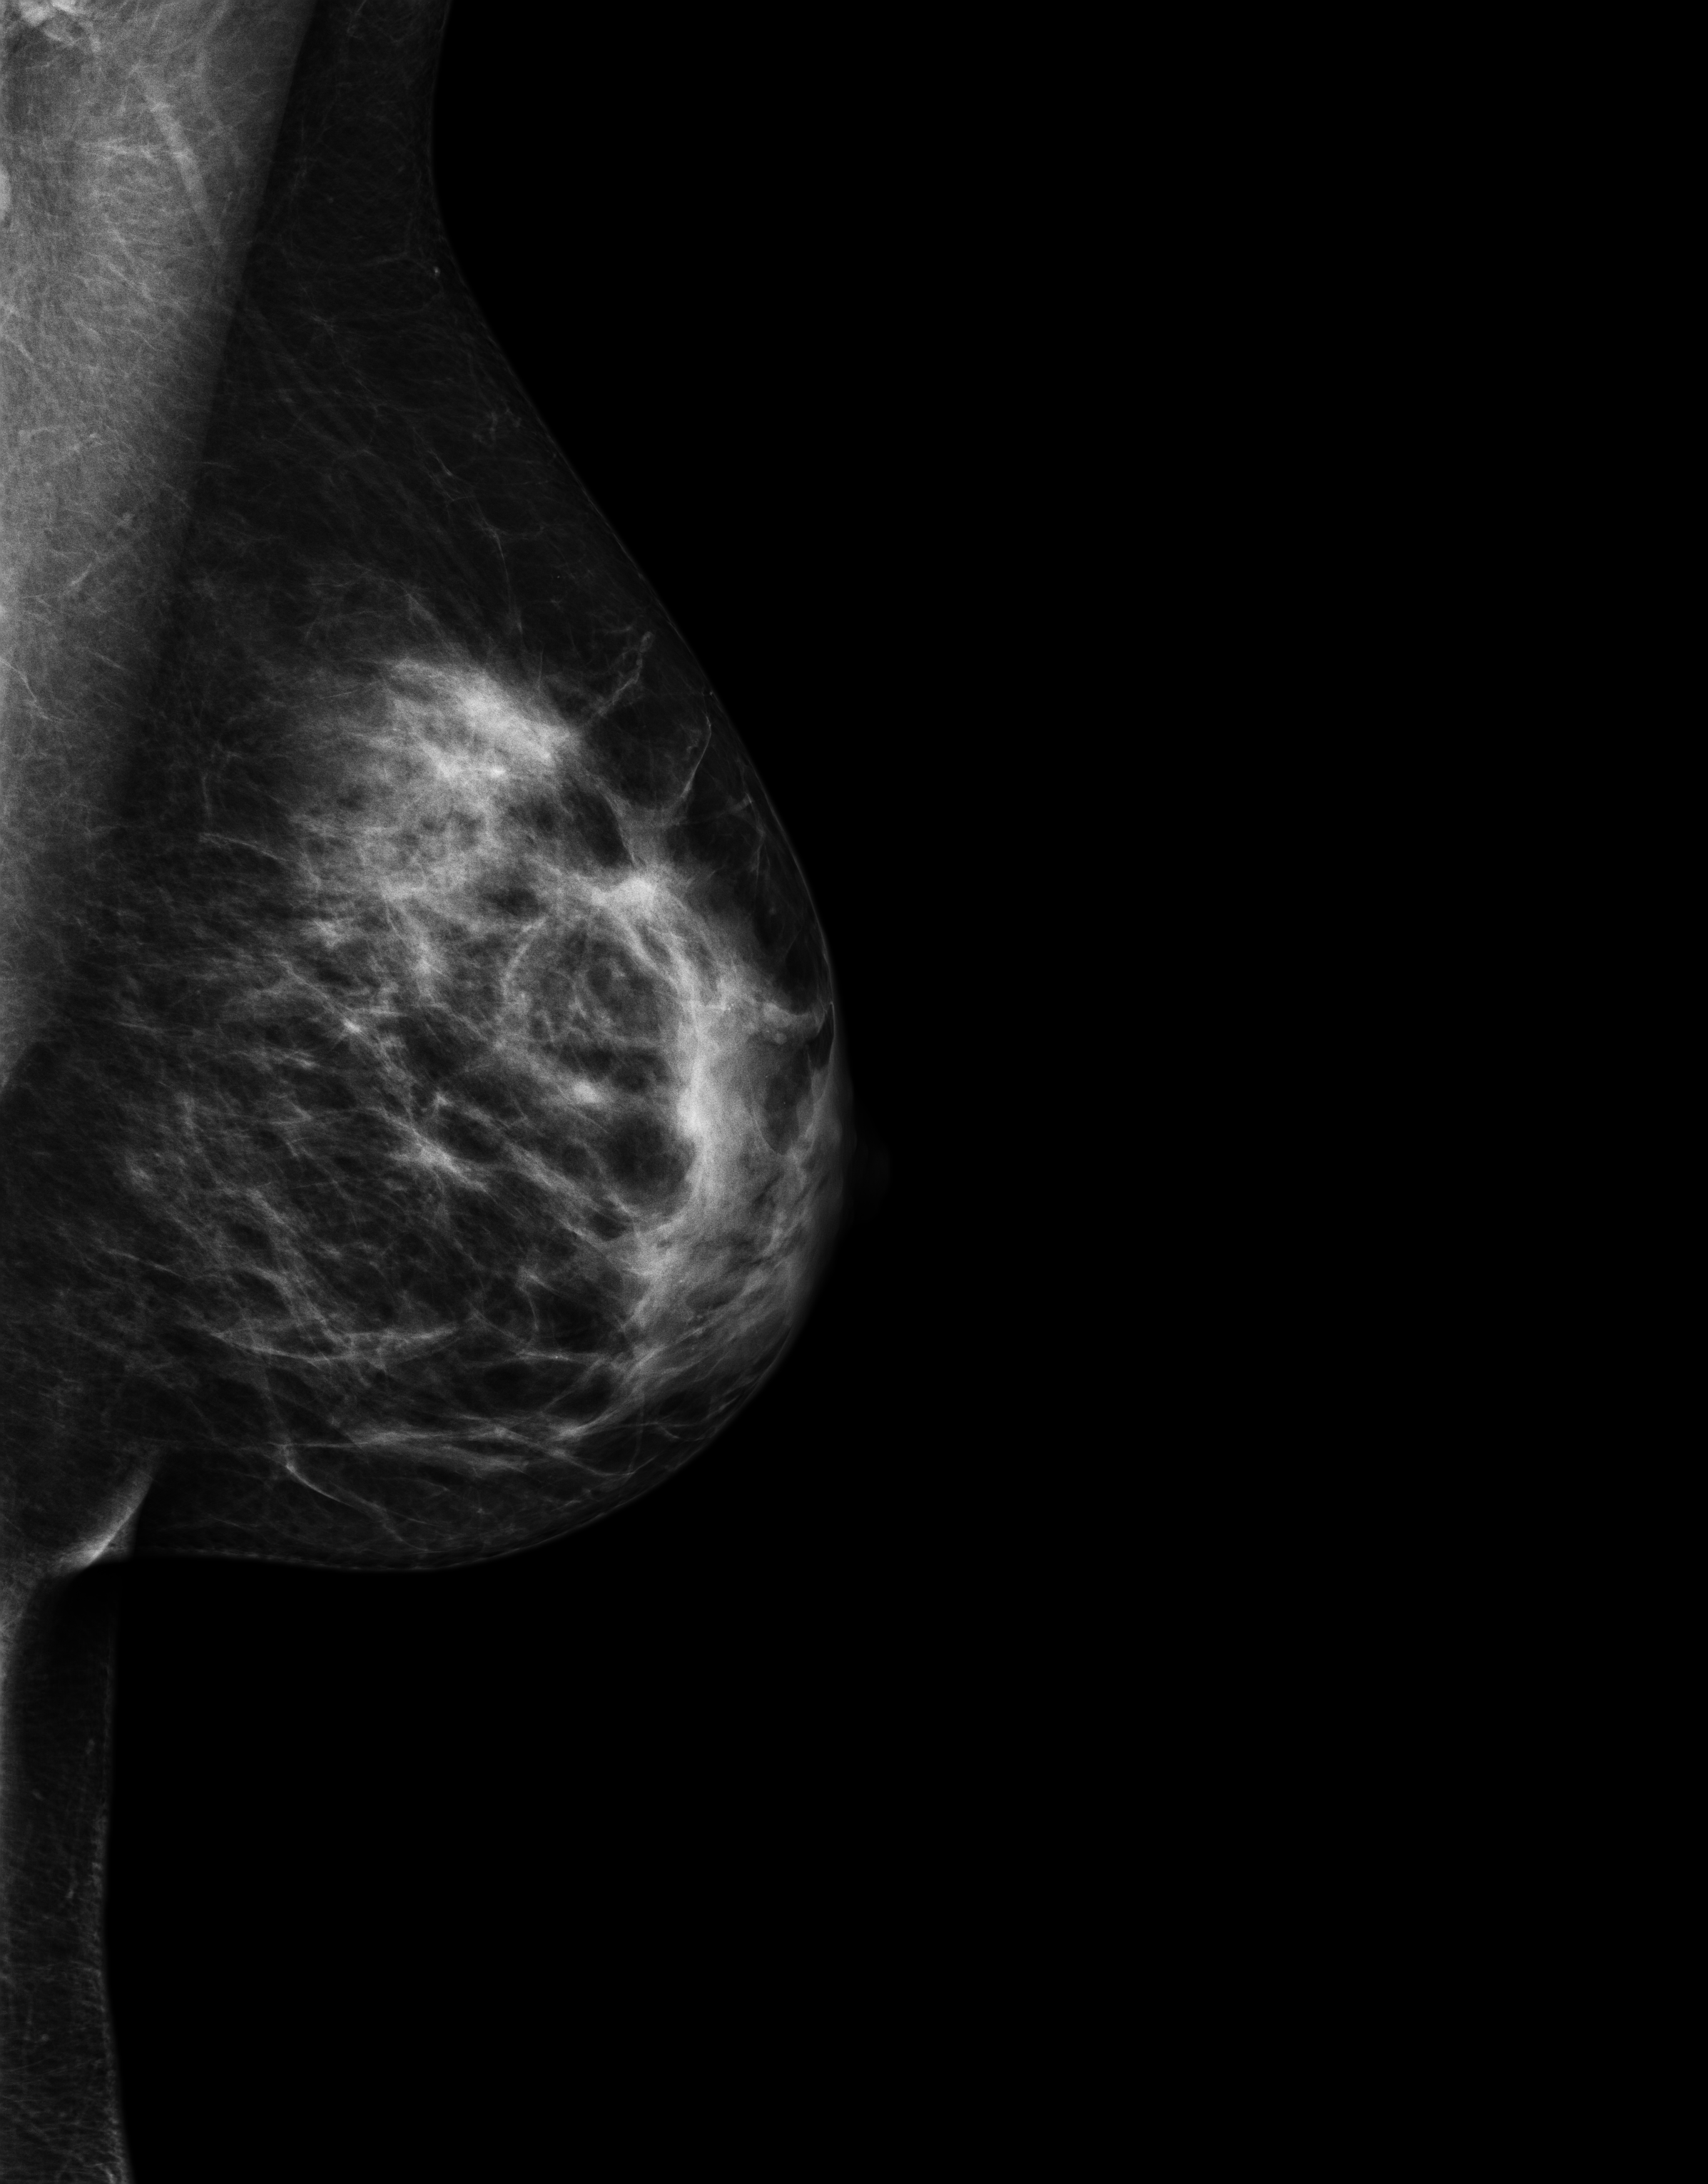
Full-field digital mammogram (FFDM); left breast; MLO view; screening examination; system: Senographe Essential ADS_56.21.3. Patient: female, 46 years.
- BI-RADS breast density category at the screening exam (both breasts, scale 1–4): 3
- final BI-RADS category for the screening round (tomosynthesis exam, both breasts): category 1
- recall: no recall after this screen